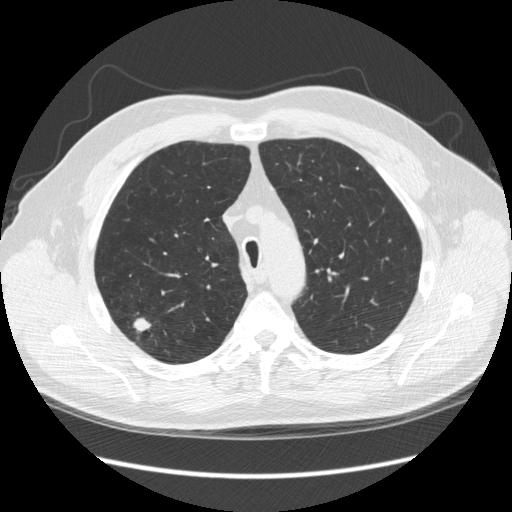
Low-dose screening chest CT, one axial slice; position 189 of 248 along the scan axis; reconstruction kernel STANDARD; 120 kVp; lung window (W 1500 / L -600 HU); 512 × 512 image matrix, field of view 380 × 380 mm.
Outlined on this slice (outlined manually by an expert reader):
- lesion 1 (tumor, upper lobe of right lung): bounding box <134,318,151,332> (left, top, right, bottom; pixels)